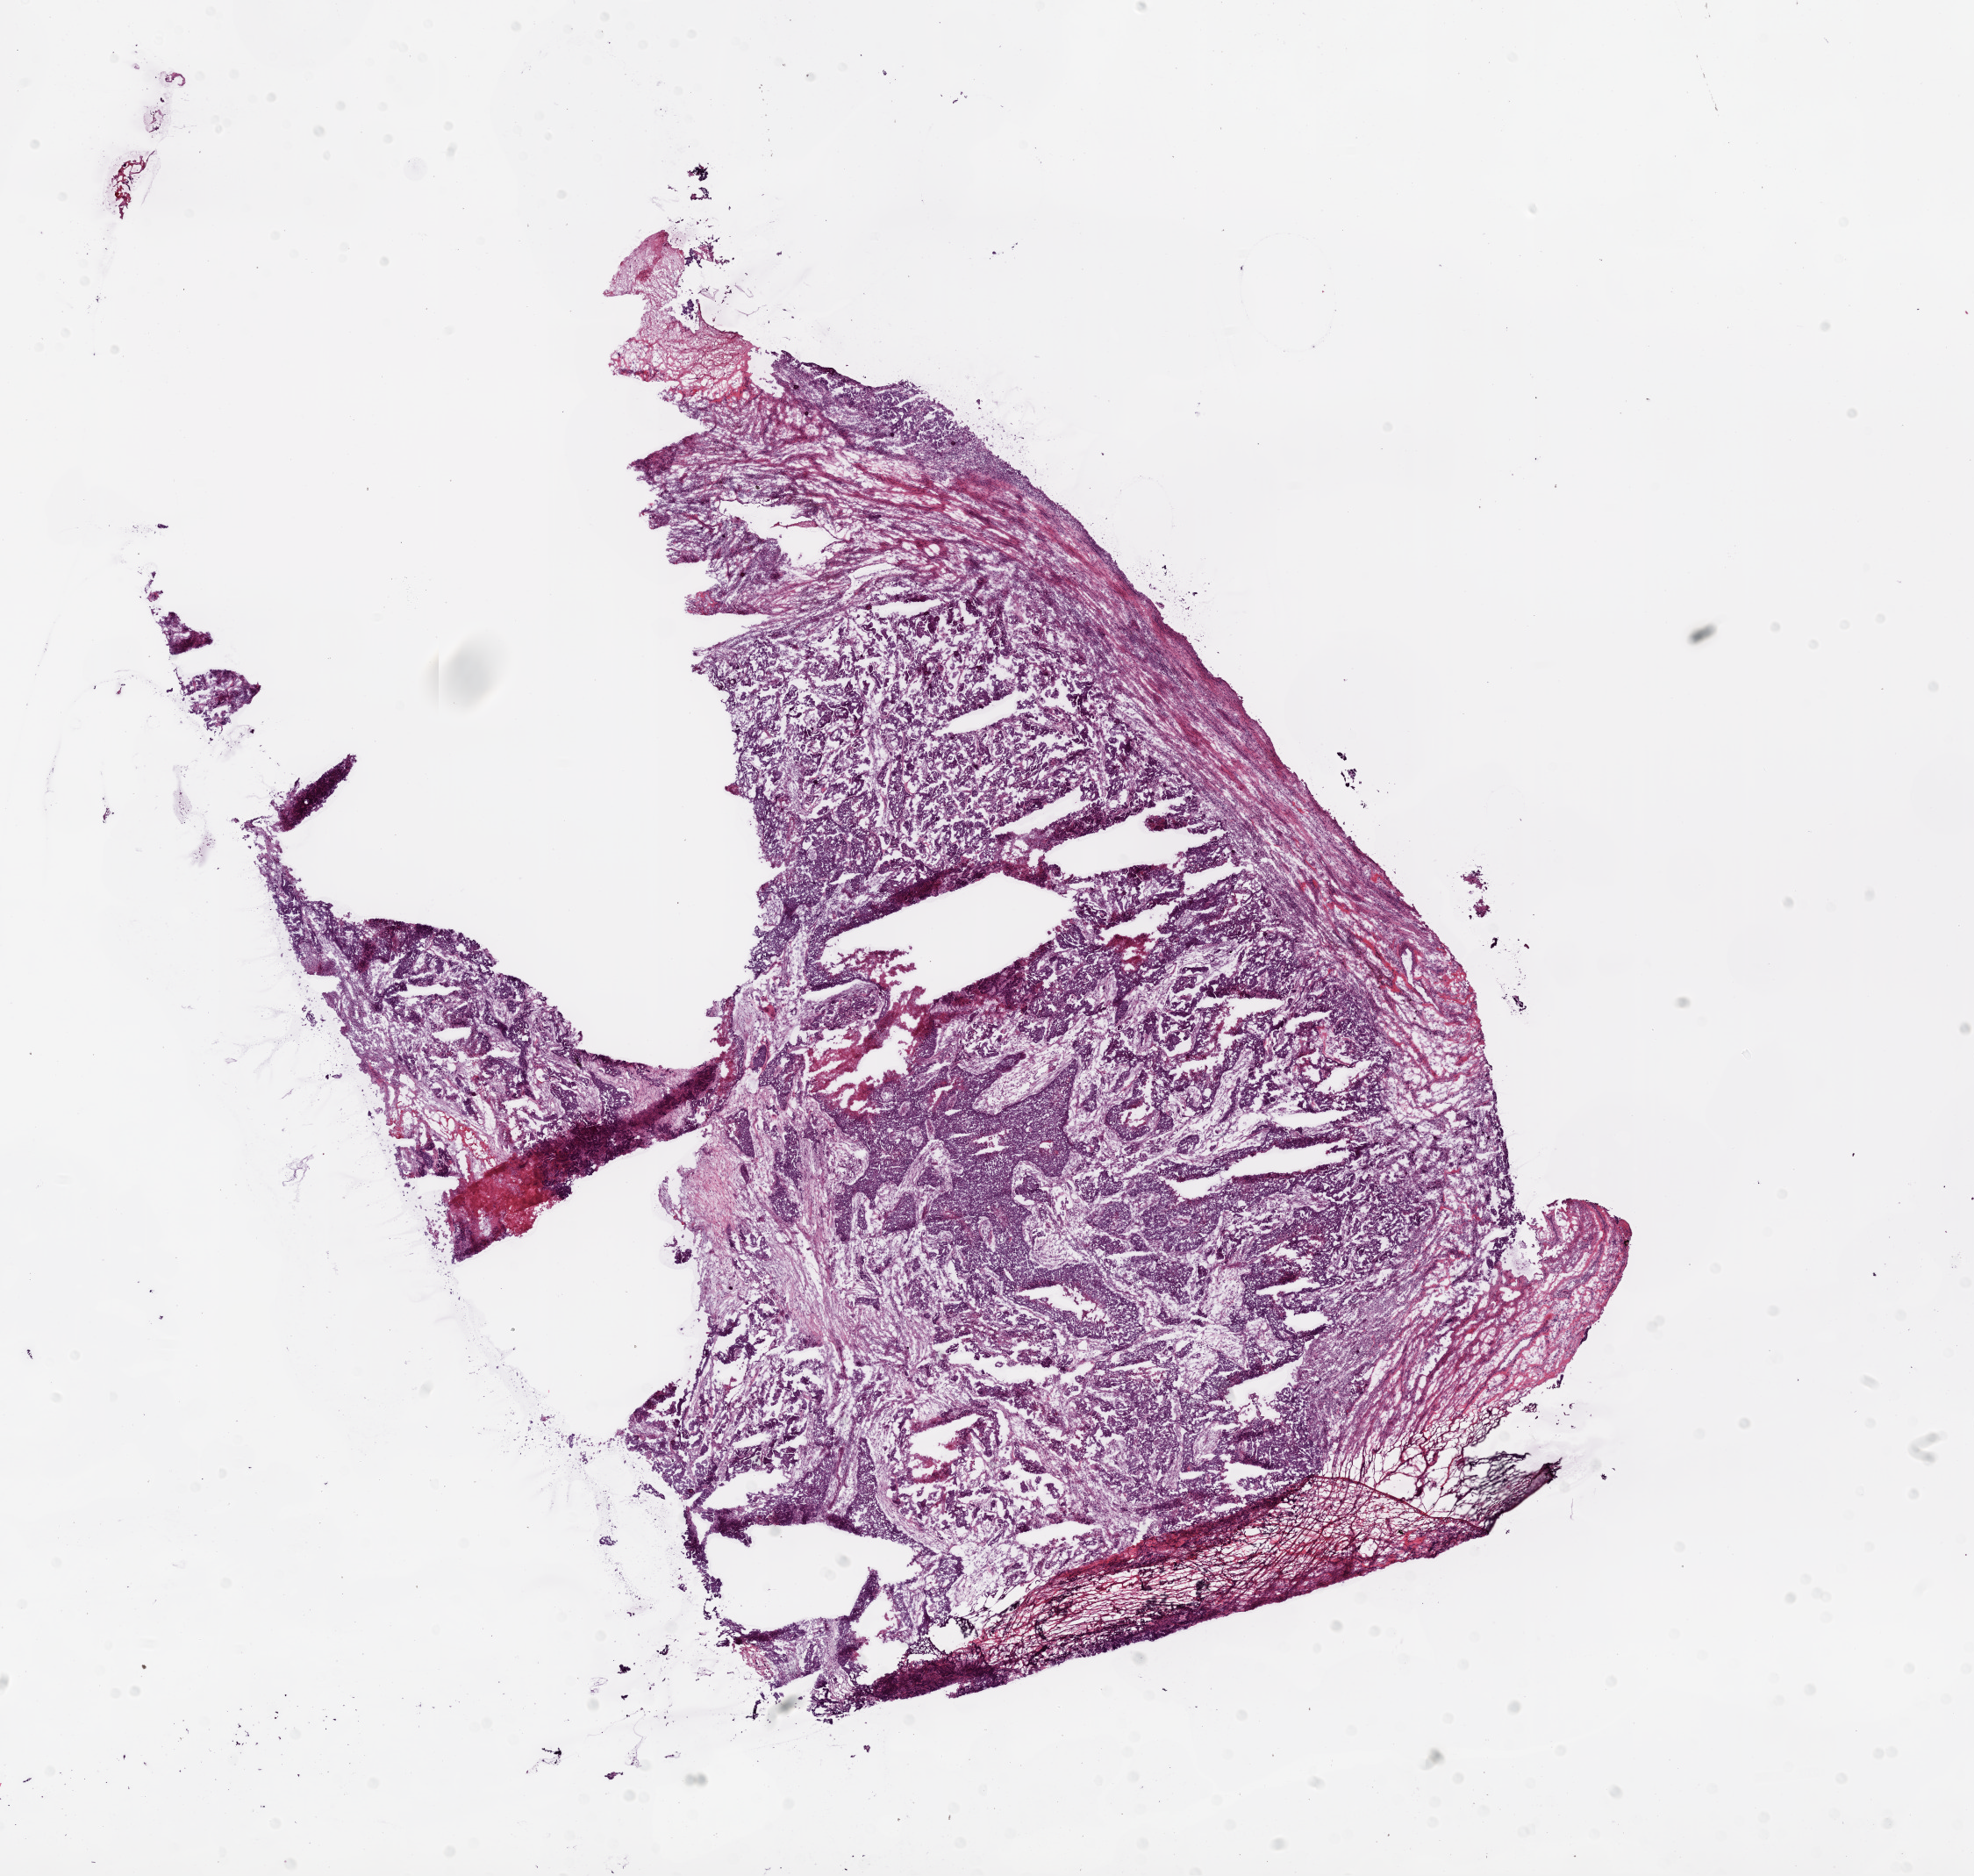
Hematoxylin and eosin (H&E) stained whole-slide image — a low-resolution overview of the entire scanned area, about 18.1 x 17.2 mm. Frozen section from the bottom of the tissue portion. Sample: primary tumour, ovary. Patient: female, age at initial diagnosis 53 years. Histologic grade: G3 (poorly differentiated). Slide review estimates, as recorded: tumour cells 70%, tumour nuclei 70%, normal cells 0%, stromal cells 30%, necrosis 0%.
Laterality: right. Diagnosis: Serous cystadenocarcinoma, NOS. FIGO stage: IIC.